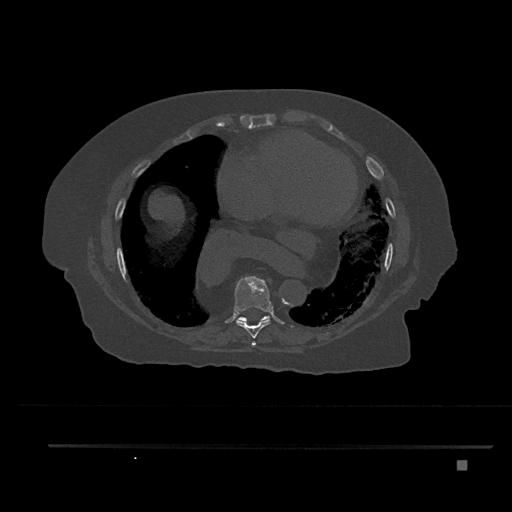
CT including the spine, one axial slice. Slice 431 of 797 in the series (ordered by position). 120 kVp. Bone window (W 1800 / L 400 HU). 0.5 mm slice thickness. 512 × 512 image matrix, field of view 437 × 437 mm. Patient: female, 76 years. From the clinical record (not read from this slice): primary cancer: lung; vertebrae with lytic lesions (as recorded): T11, L3.
Outlined on this slice (semi-automatically segmented with operator editing):
- T7 vertebra: bounding box (x1, y1, x2, y2) in pixels: (252, 342, 256, 346)
- T8 vertebra: (234, 276, 271, 347)
- T9 vertebra: (237, 316, 270, 322)